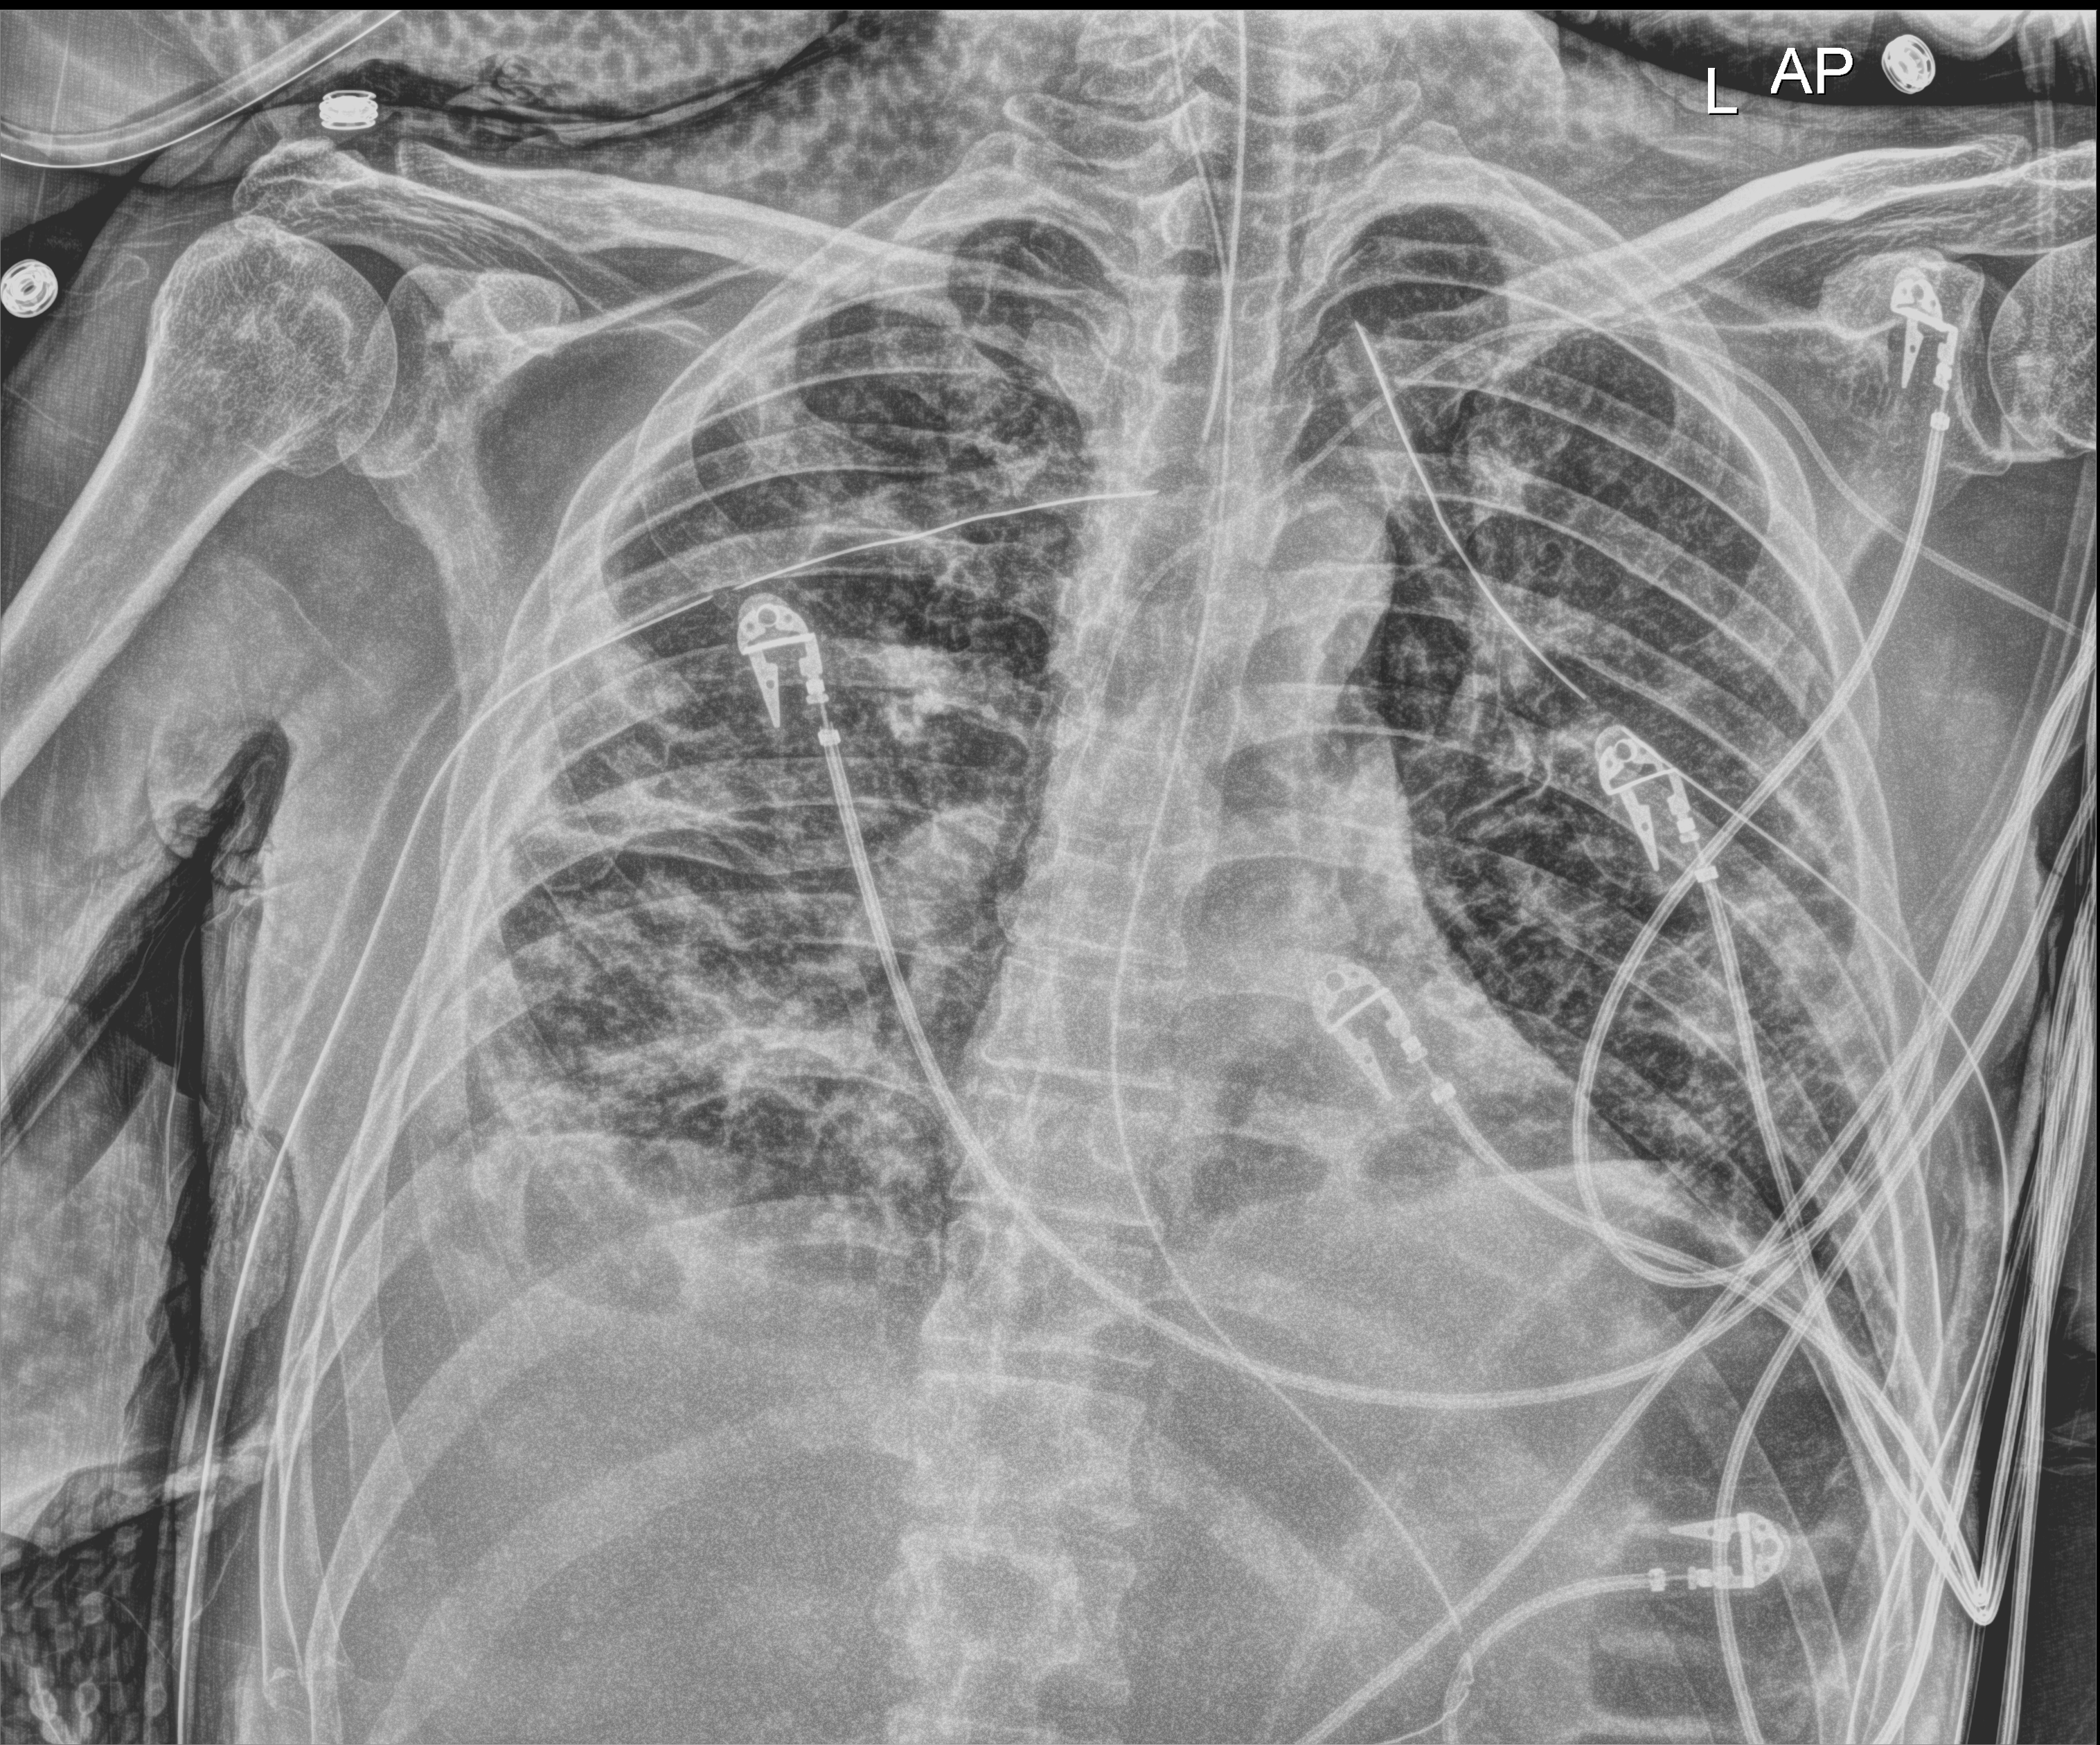
Portable chest radiograph, anteroposterior (AP) projection. Patient hospitalised with COVID-19; male, aged 18–59 years.
Admission-level facts for this patient (not findings on this image; timing relative to this image not recorded): admitted to intensive care during this hospital stay: yes; hypertension (admission record): yes; length of hospital stay: 96 days.